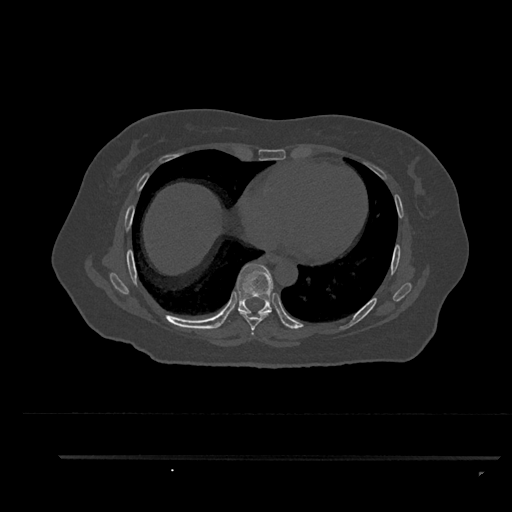
CT including the spine, one axial slice. Slice 485 of 797 in the series (ordered by position). 120 kVp. Bone window (W 1800 / L 400 HU). 0.5 mm slice thickness. 512 × 512 image matrix, field of view 408 × 408 mm. Patient: female, 44 years. From the clinical record (not read from this slice): primary cancer: renal.
Structures marked on this image (semi-automatic segmentation, software-assisted and operator-edited):
- T7 vertebra: box from (x=239, y=311) to (x=271, y=335) px
- T8 vertebra: (x=236, y=263)–(x=281, y=320)